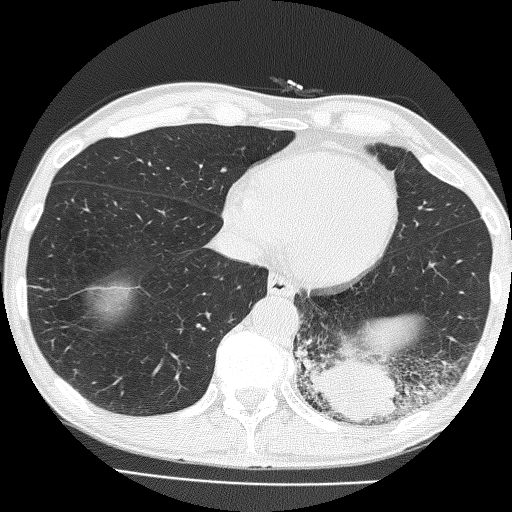
Low-dose screening chest CT, one axial slice; slice 51 of 160 in the series (ordered by position); lung window (W 1500 / L -600 HU); 2 mm slice thickness; 512 × 512 image matrix.
Annotated regions visible in this slice (expert manual segmentation):
- lesion 1 (tumor, lower lobe of left lung): box from (x=296, y=348) to (x=400, y=424) px